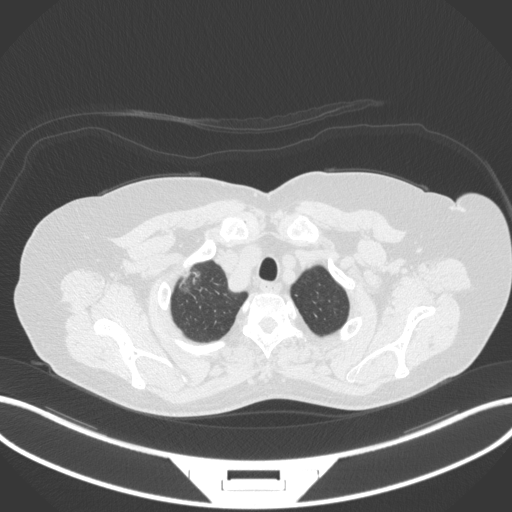
Chest CT, one axial slice; reconstruction kernel B31f; 120 kVp; lung window (W 1500 / L -600 HU); 512 × 512 image matrix, field of view 400 × 400 mm. Patient: female, 62 years. Case-level facts recorded for this patient, not image findings: clinical TNM (as recorded): T1c N0 M0.
Annotated regions visible in this slice (bounding box drawn by a radiologist):
- lung tumour (recorded histology: adenocarcinoma): bounding box [x1, y1, x2, y2] px = [176, 265, 210, 300]